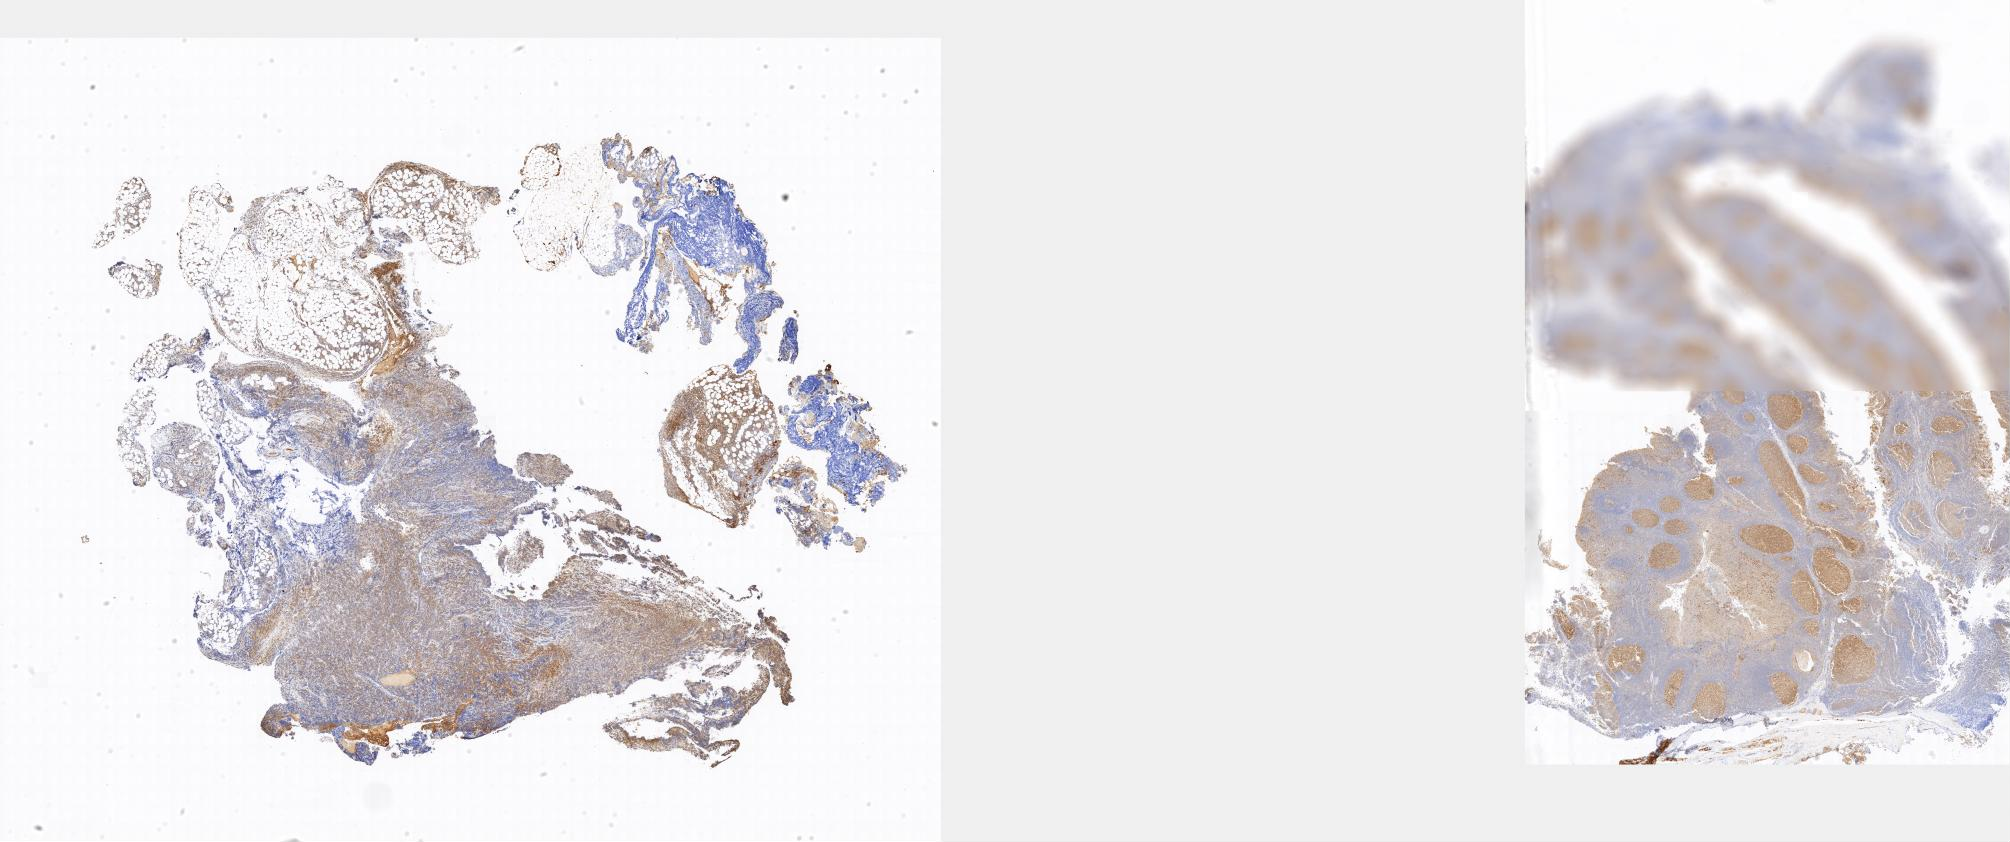
Whole-slide image, immunohistochemical stain for BCL6 — low-resolution overview of the scanned area, specimen: tumor tissue, anatomic site: abdominal lymph node. Male, age 9 years at initial diagnosis.
Diagnosis: Burkitt lymphoma, NOS.